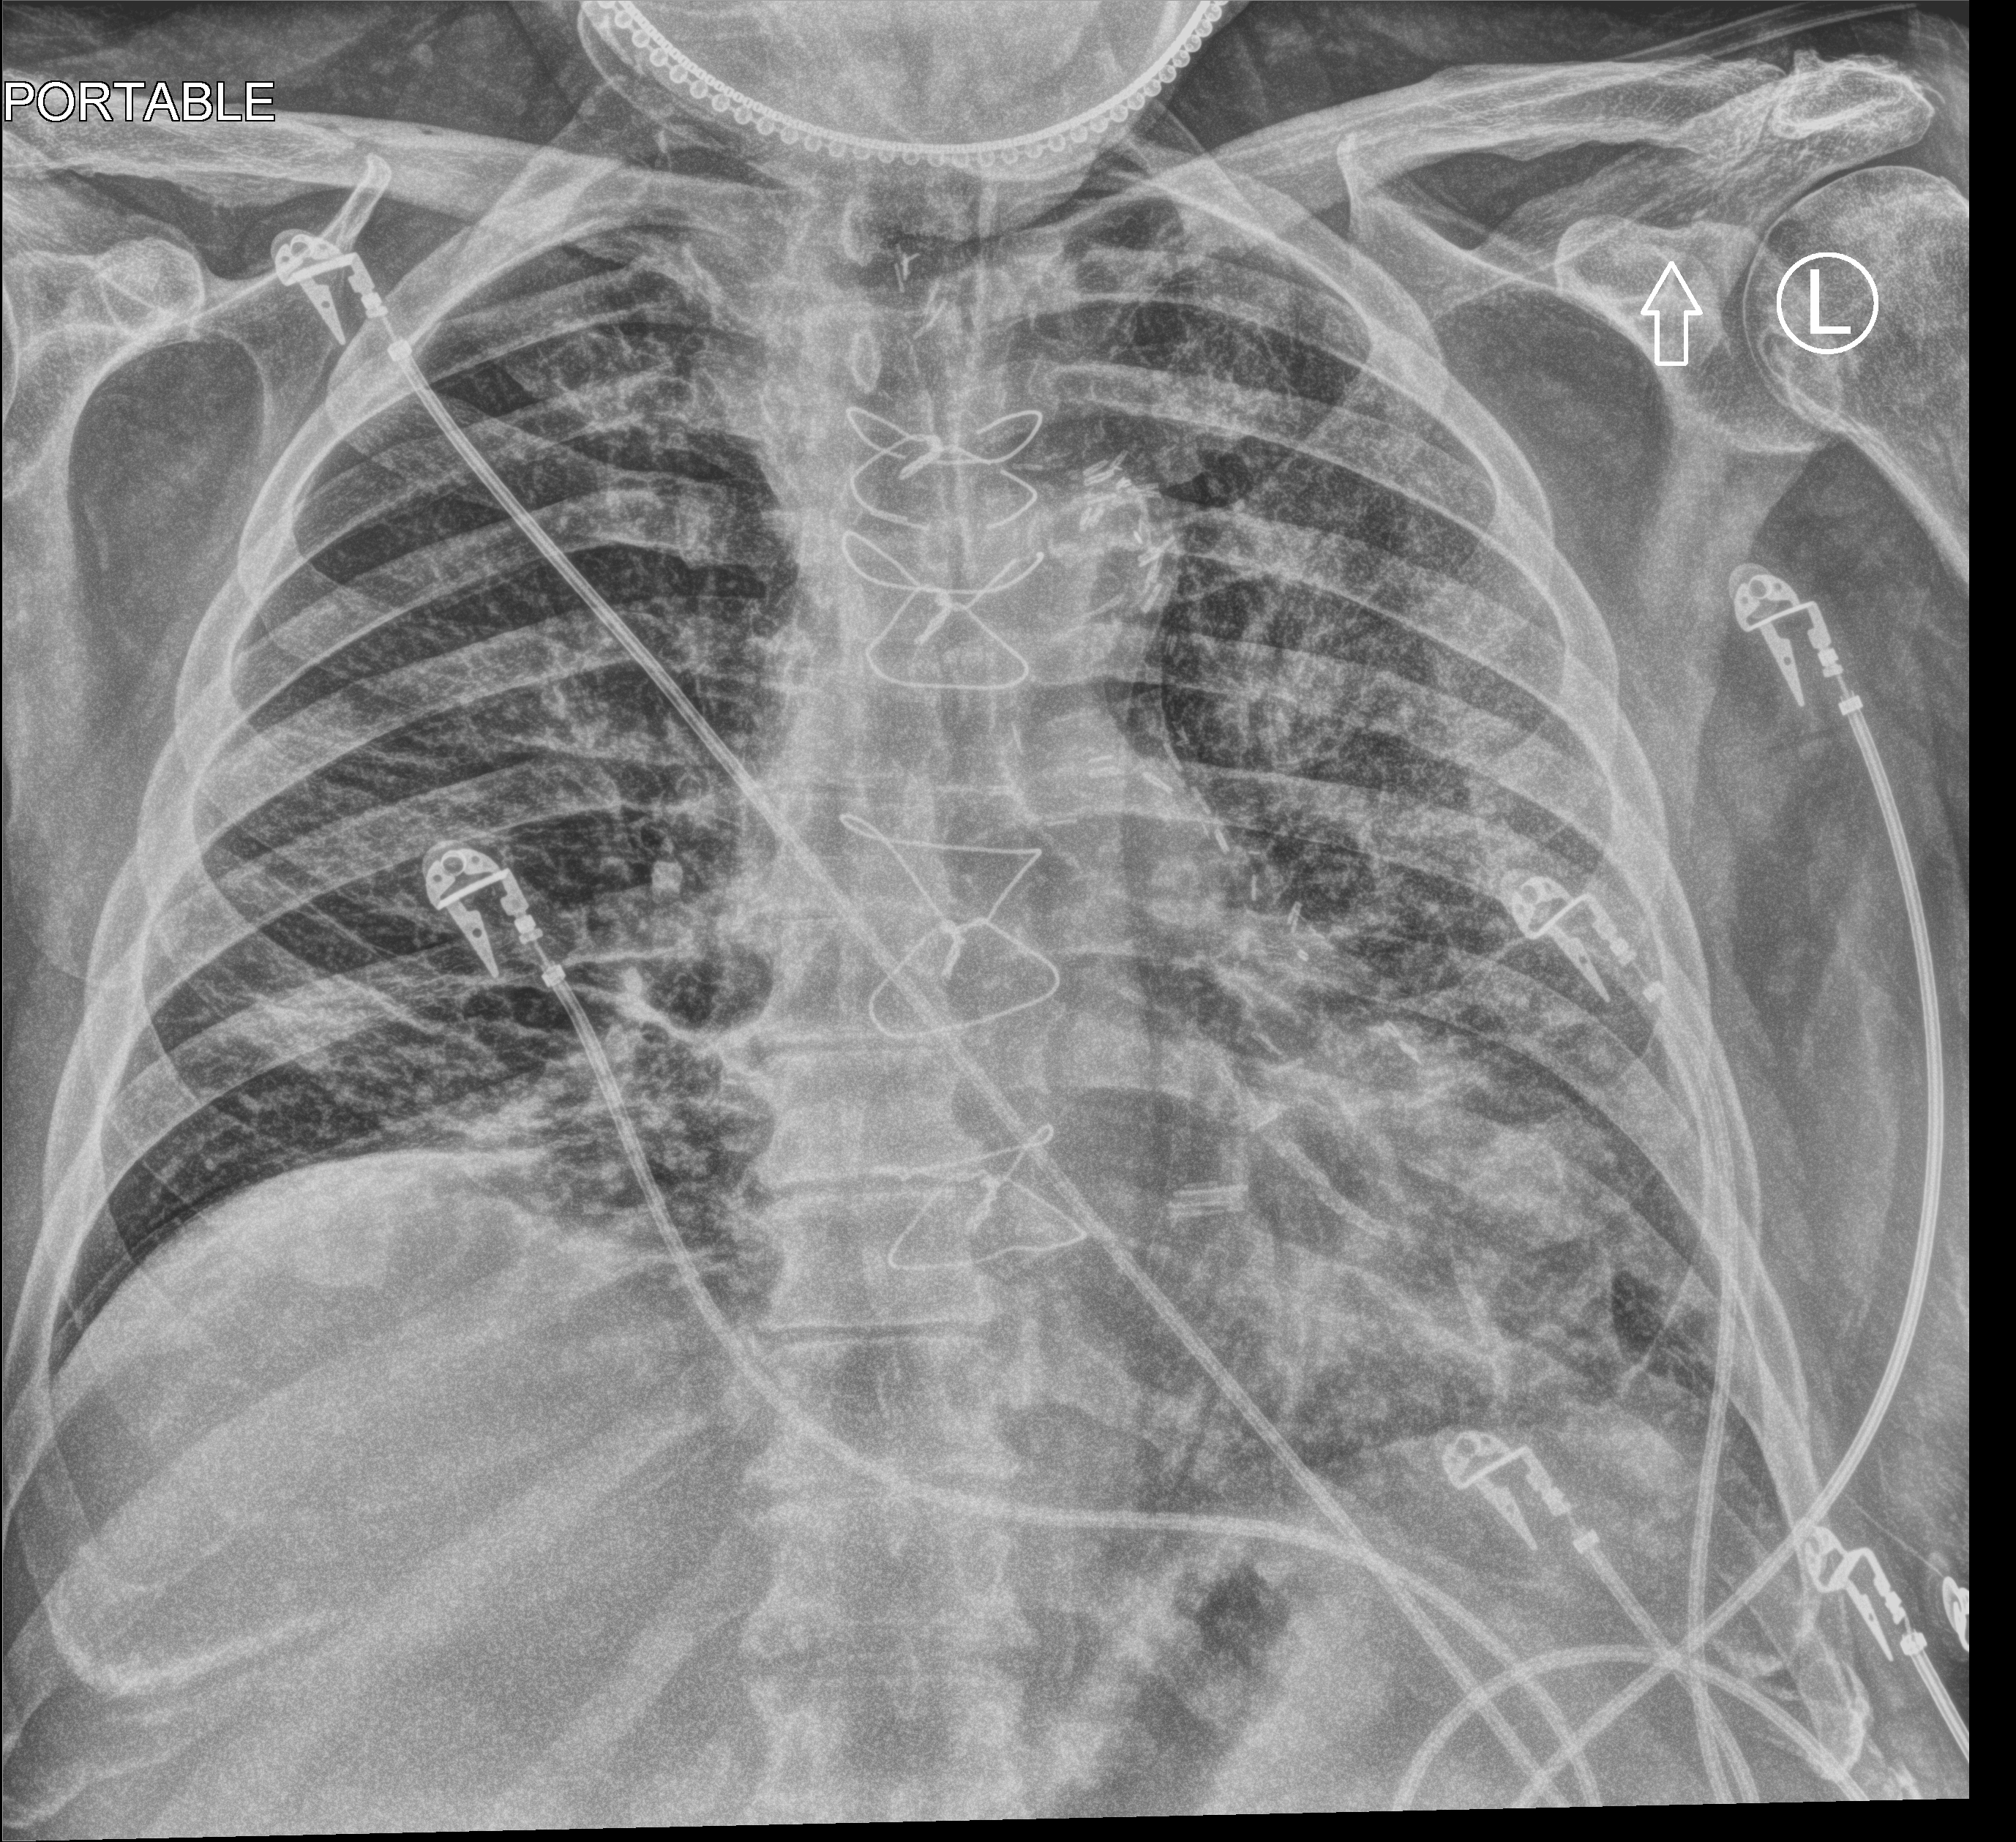
Bedside chest radiograph (computed radiography); anteroposterior (AP) projection. Patient hospitalised with COVID-19; male, aged 60–74 years.
From the hospital-stay record, not from the radiograph (when in the stay this image was taken is not recorded):
- mechanically ventilated during this hospital stay: yes
- admitted to intensive care during this hospital stay: yes
- other chronic lung disease (admission record): no